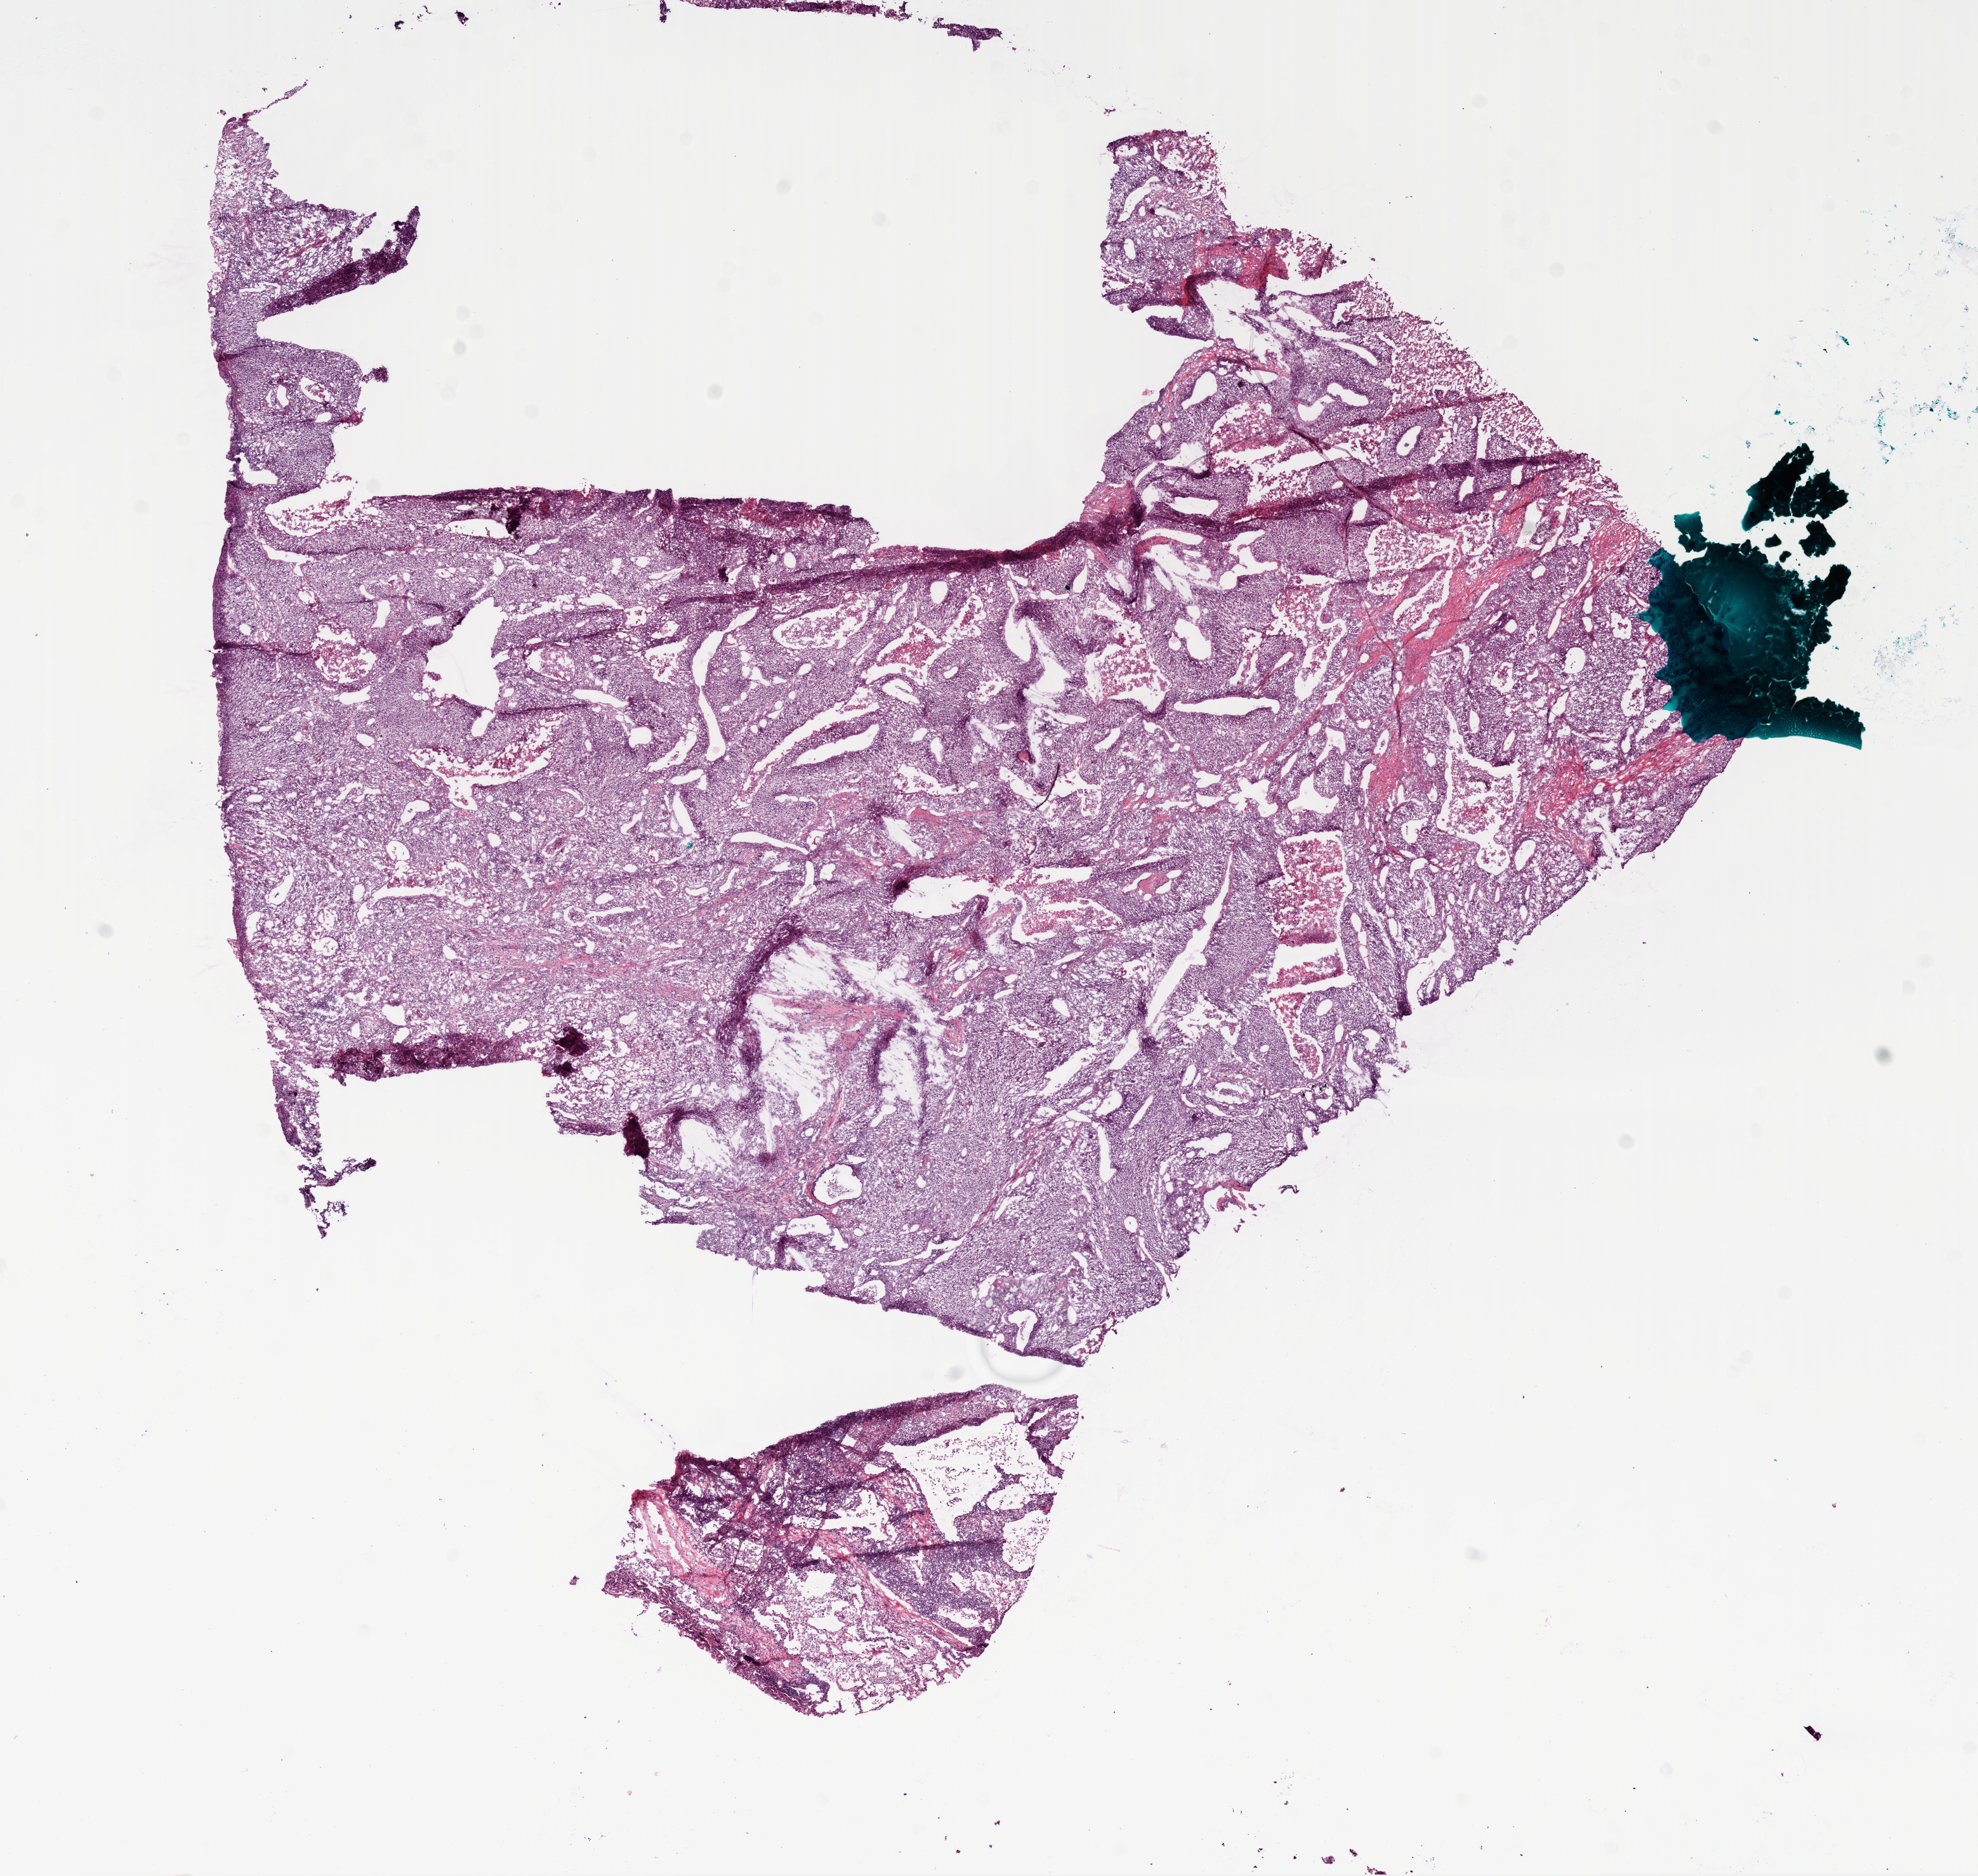
H&E whole-slide image, whole scanned area (about 12.6 x 11.9 mm, acquisition: 20x scan) shown as a low-resolution overview; frozen section; primary tumour sample from the lung. Patient: female, age at initial diagnosis 60 years. Composition of this section per pathologist review: tumour nuclei 95%, necrosis 5%.
- AJCC pathologic stage: IIIA
- diagnosis: Squamous cell carcinoma, NOS (upper lobe, lung)
- laterality: left